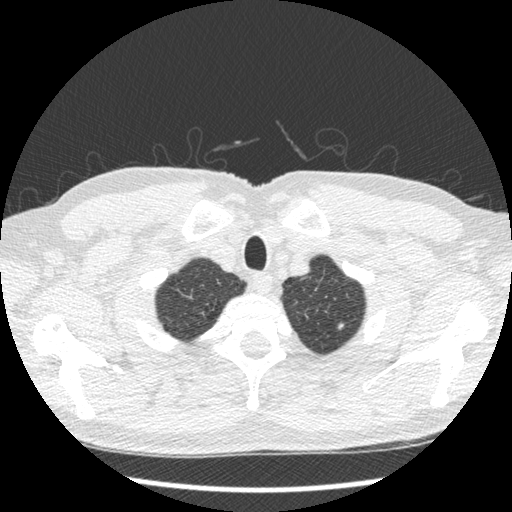
Low-dose screening chest CT, one axial slice. Reconstruction kernel STANDARD. 120 kVp. Lung window (W 1500 / L -600 HU). 1.25 mm slice thickness. 512 × 512 image matrix, field of view 340 × 340 mm.
Outlined on this slice (manually delineated by an expert):
- lesion 1 (nodule, upper lobe of left lung): box from (x=338, y=323) to (x=344, y=330) px